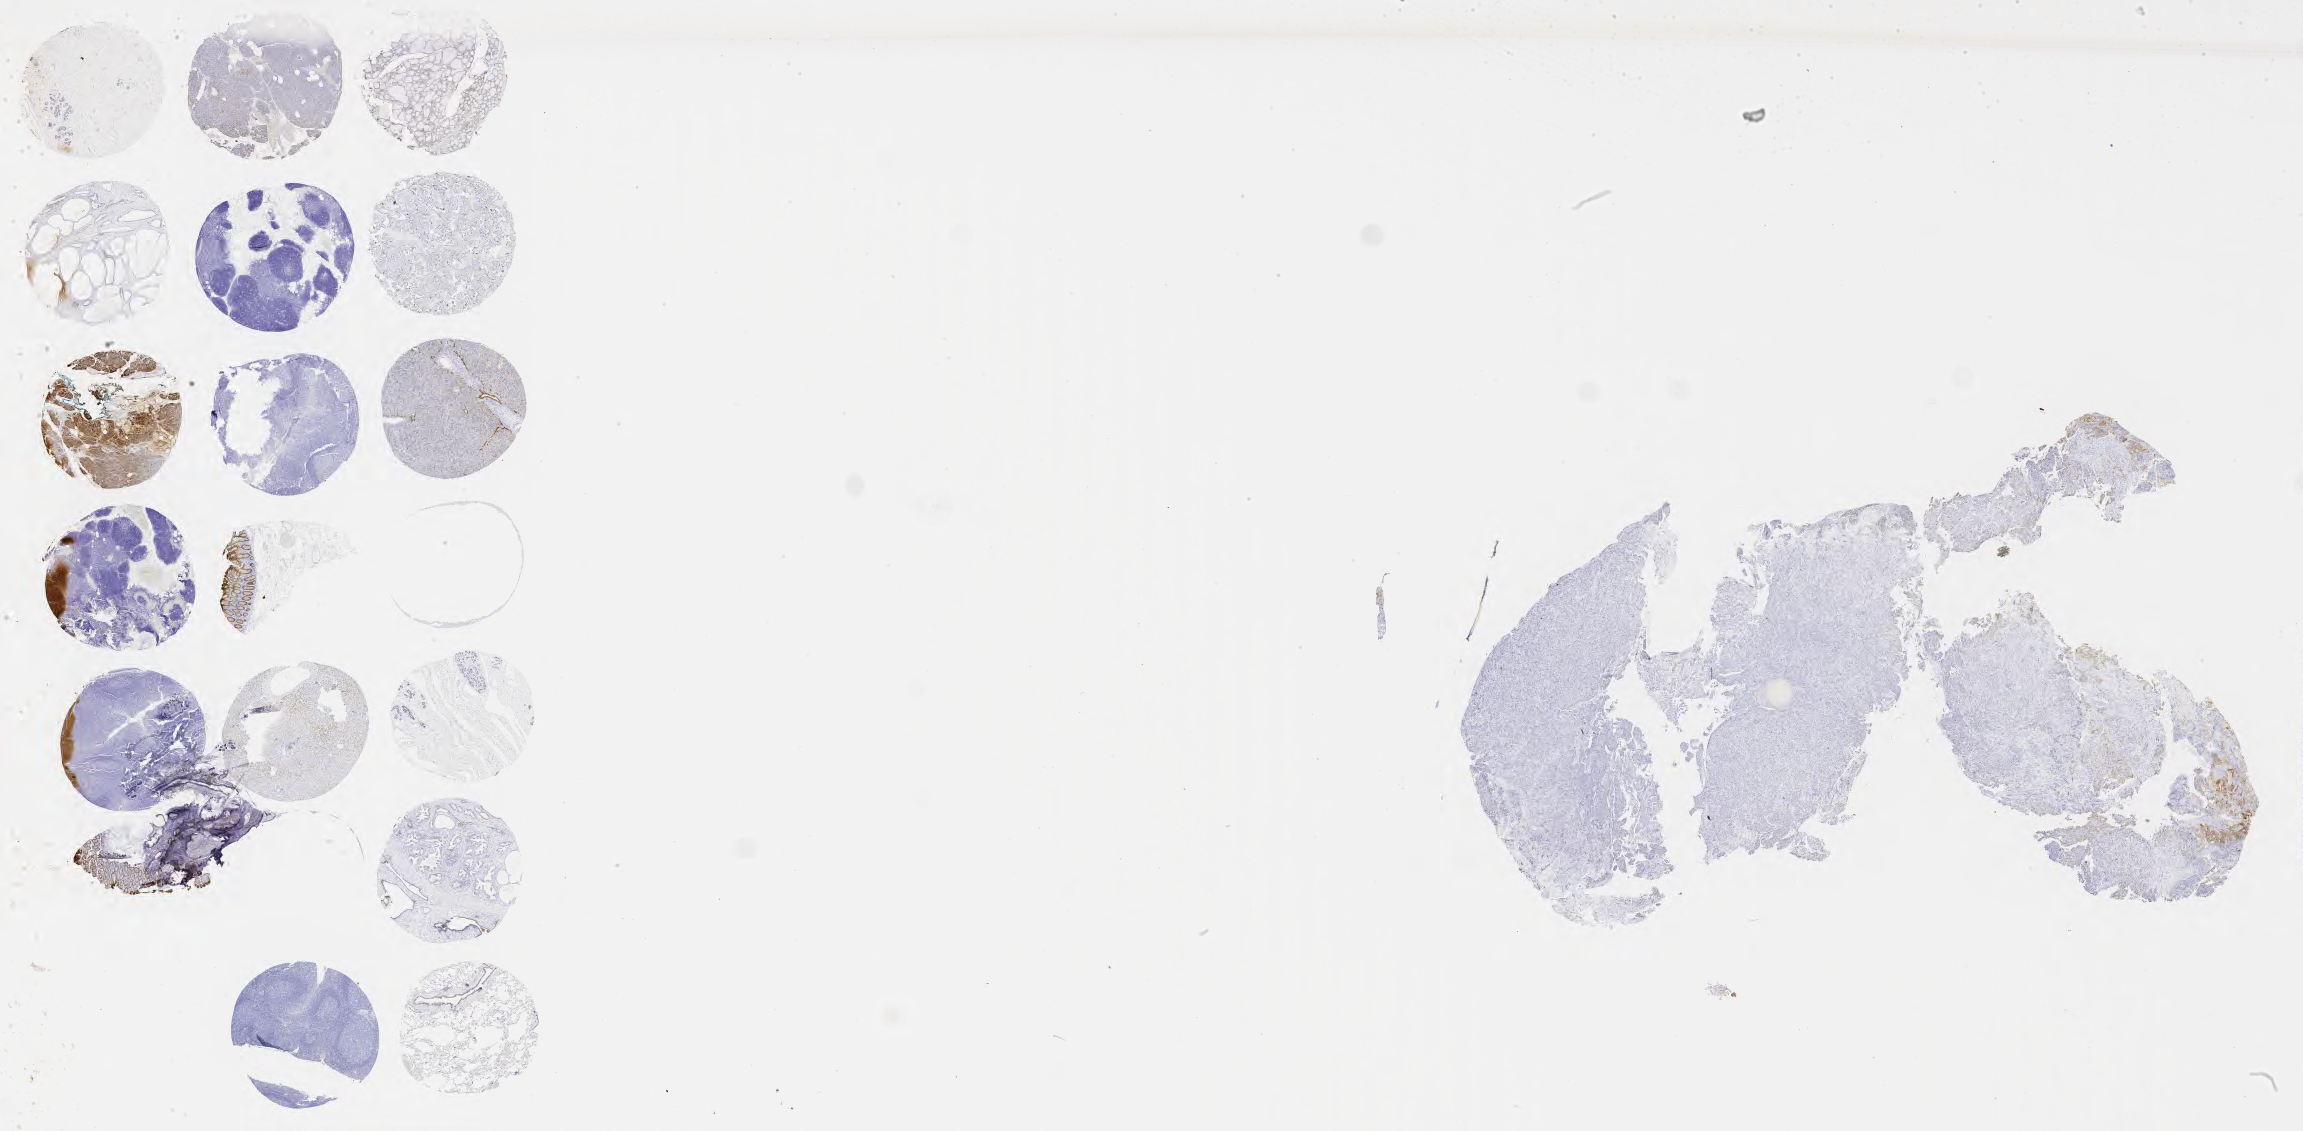
Whole-slide image, immunohistochemical stain for MOC-31 (anti-EpCAM), shown as a low-resolution overview of the whole scanned area (about 37.2 x 18.3 mm), specimen: tumor tissue, anatomic site: cervix. Patient female; age 54 years.
Diagnosis: Adenocarcinoma, NOS.